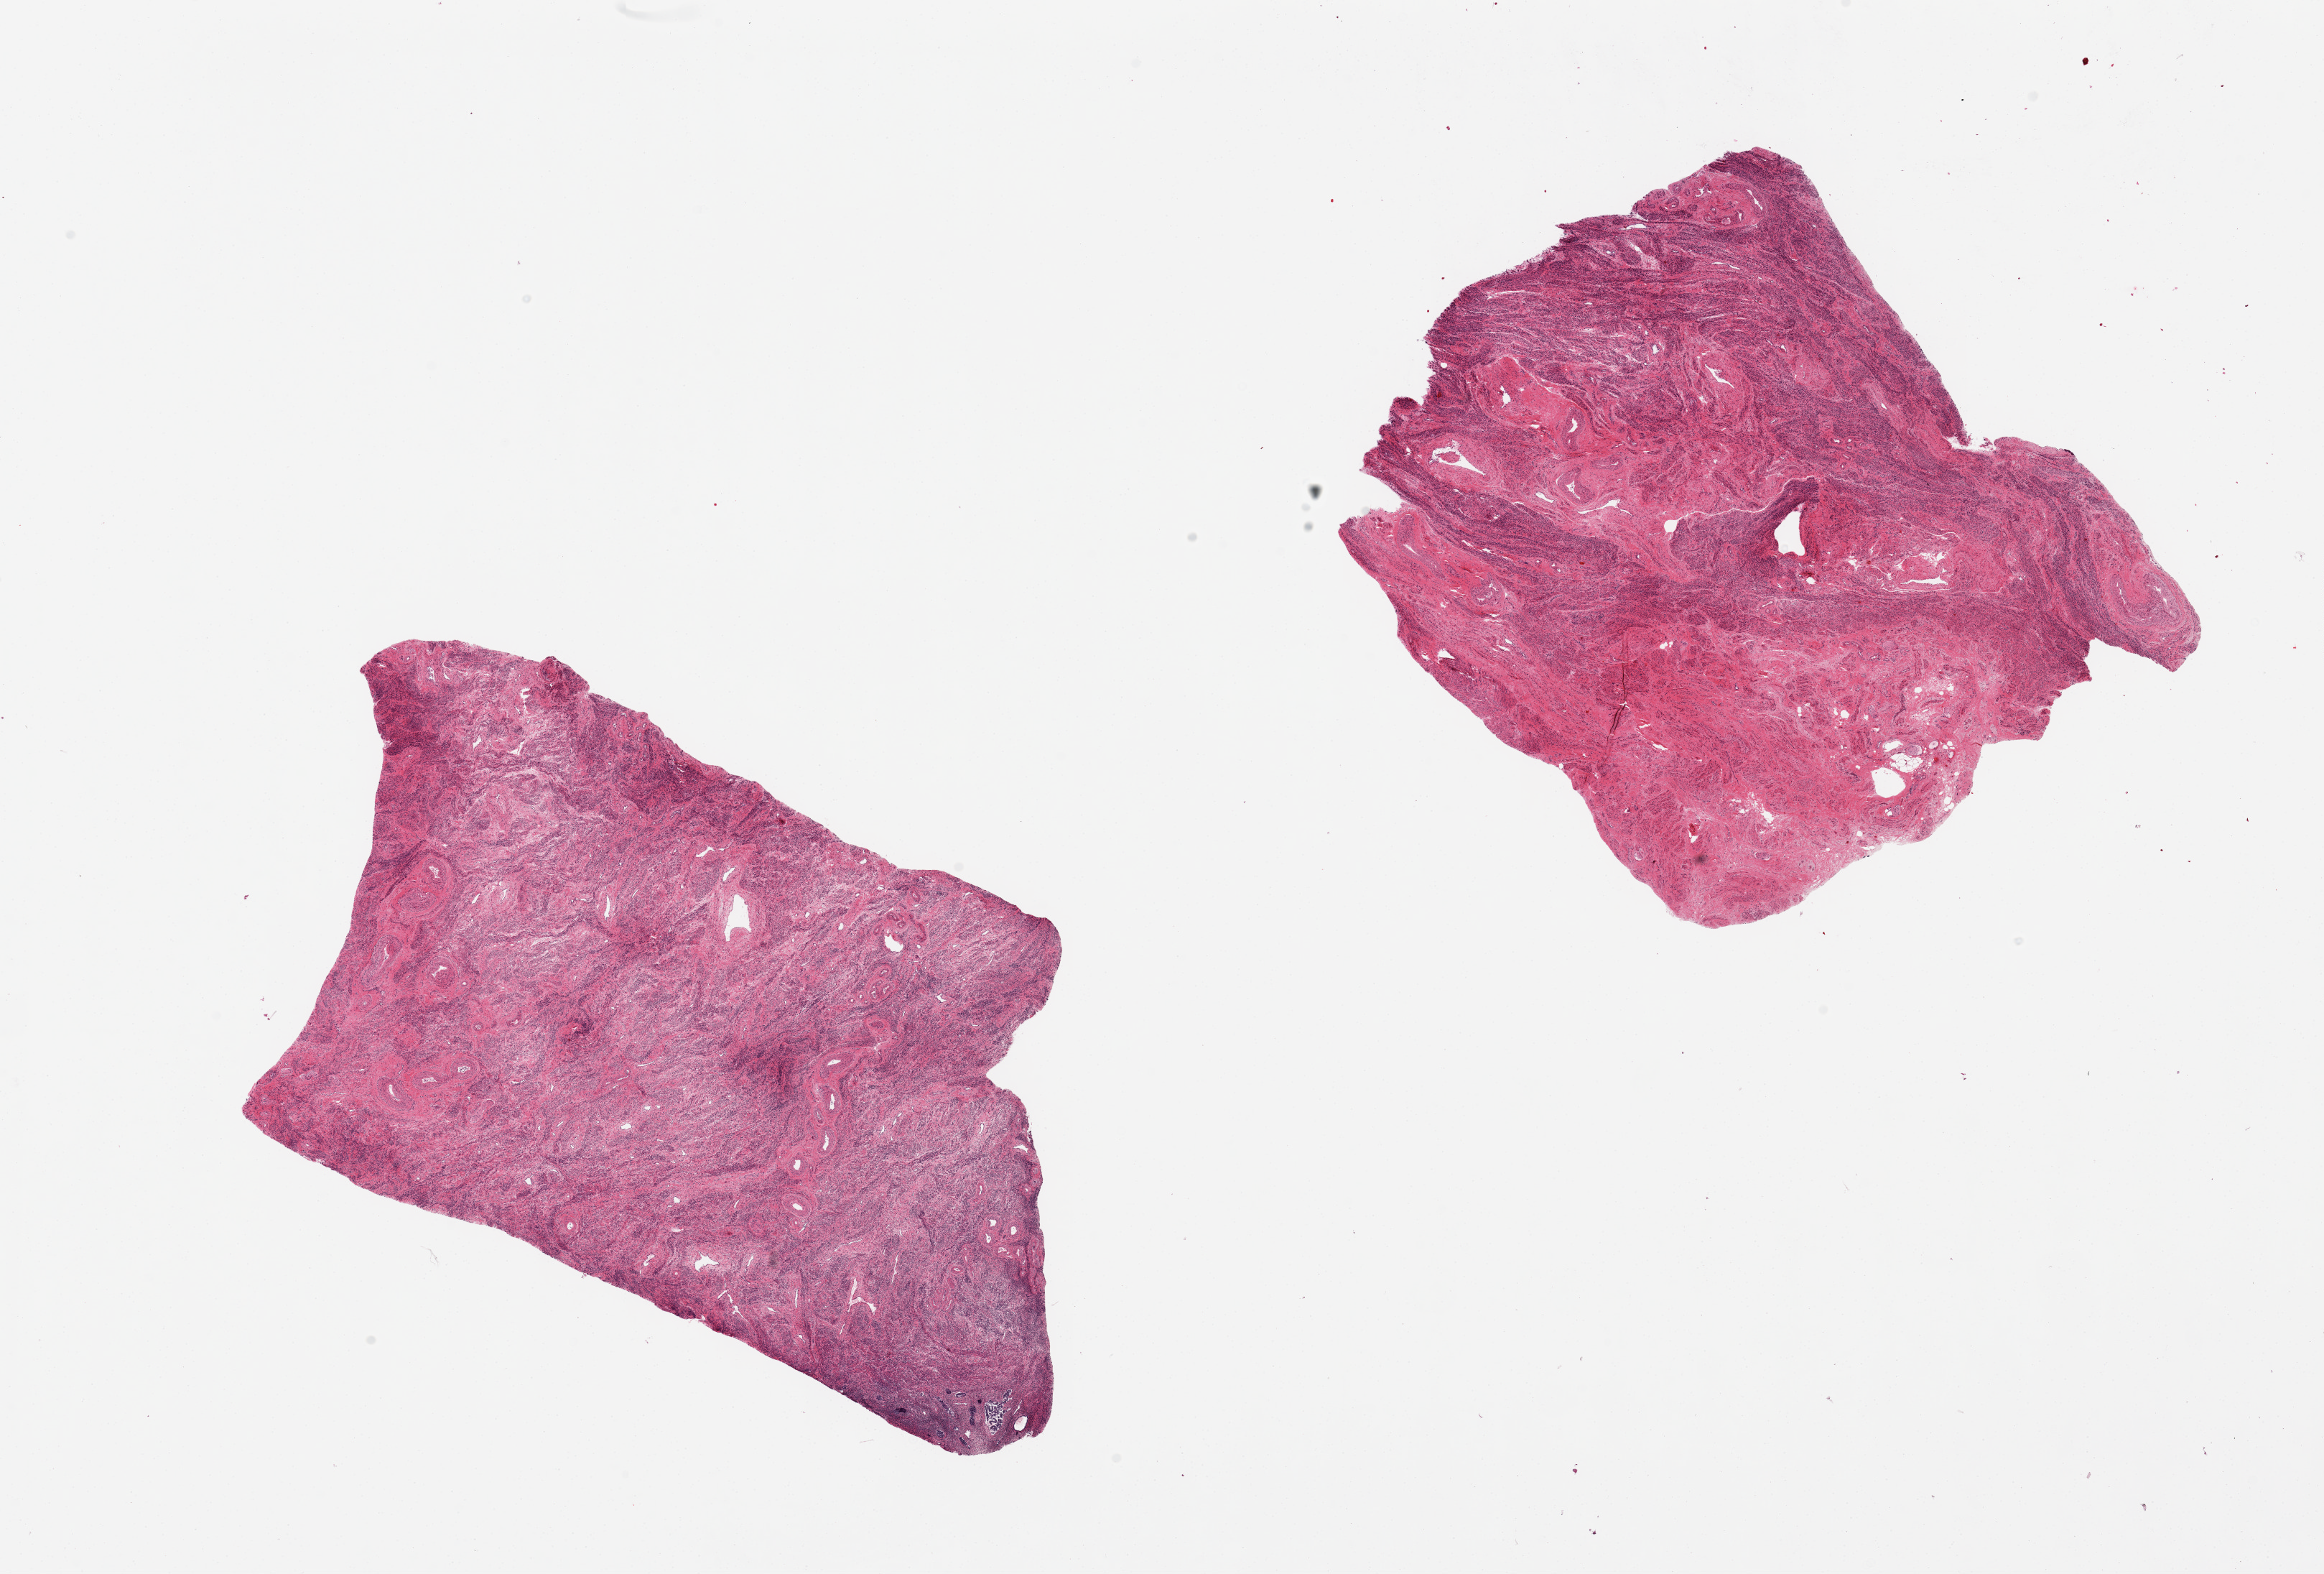
Hematoxylin and eosin (H&E) whole-slide image — shown as a low-resolution overview of the whole scanned area (about 25.6 x 17.3 mm, slide scanned at 20x). PAXgene-fixed, paraffin-embedded tissue. Section of uterus (target tissue). Tissue donor sample. Female donor.
Review note (as recorded): 2 pieces, myometrium, no viable endometrium noted.